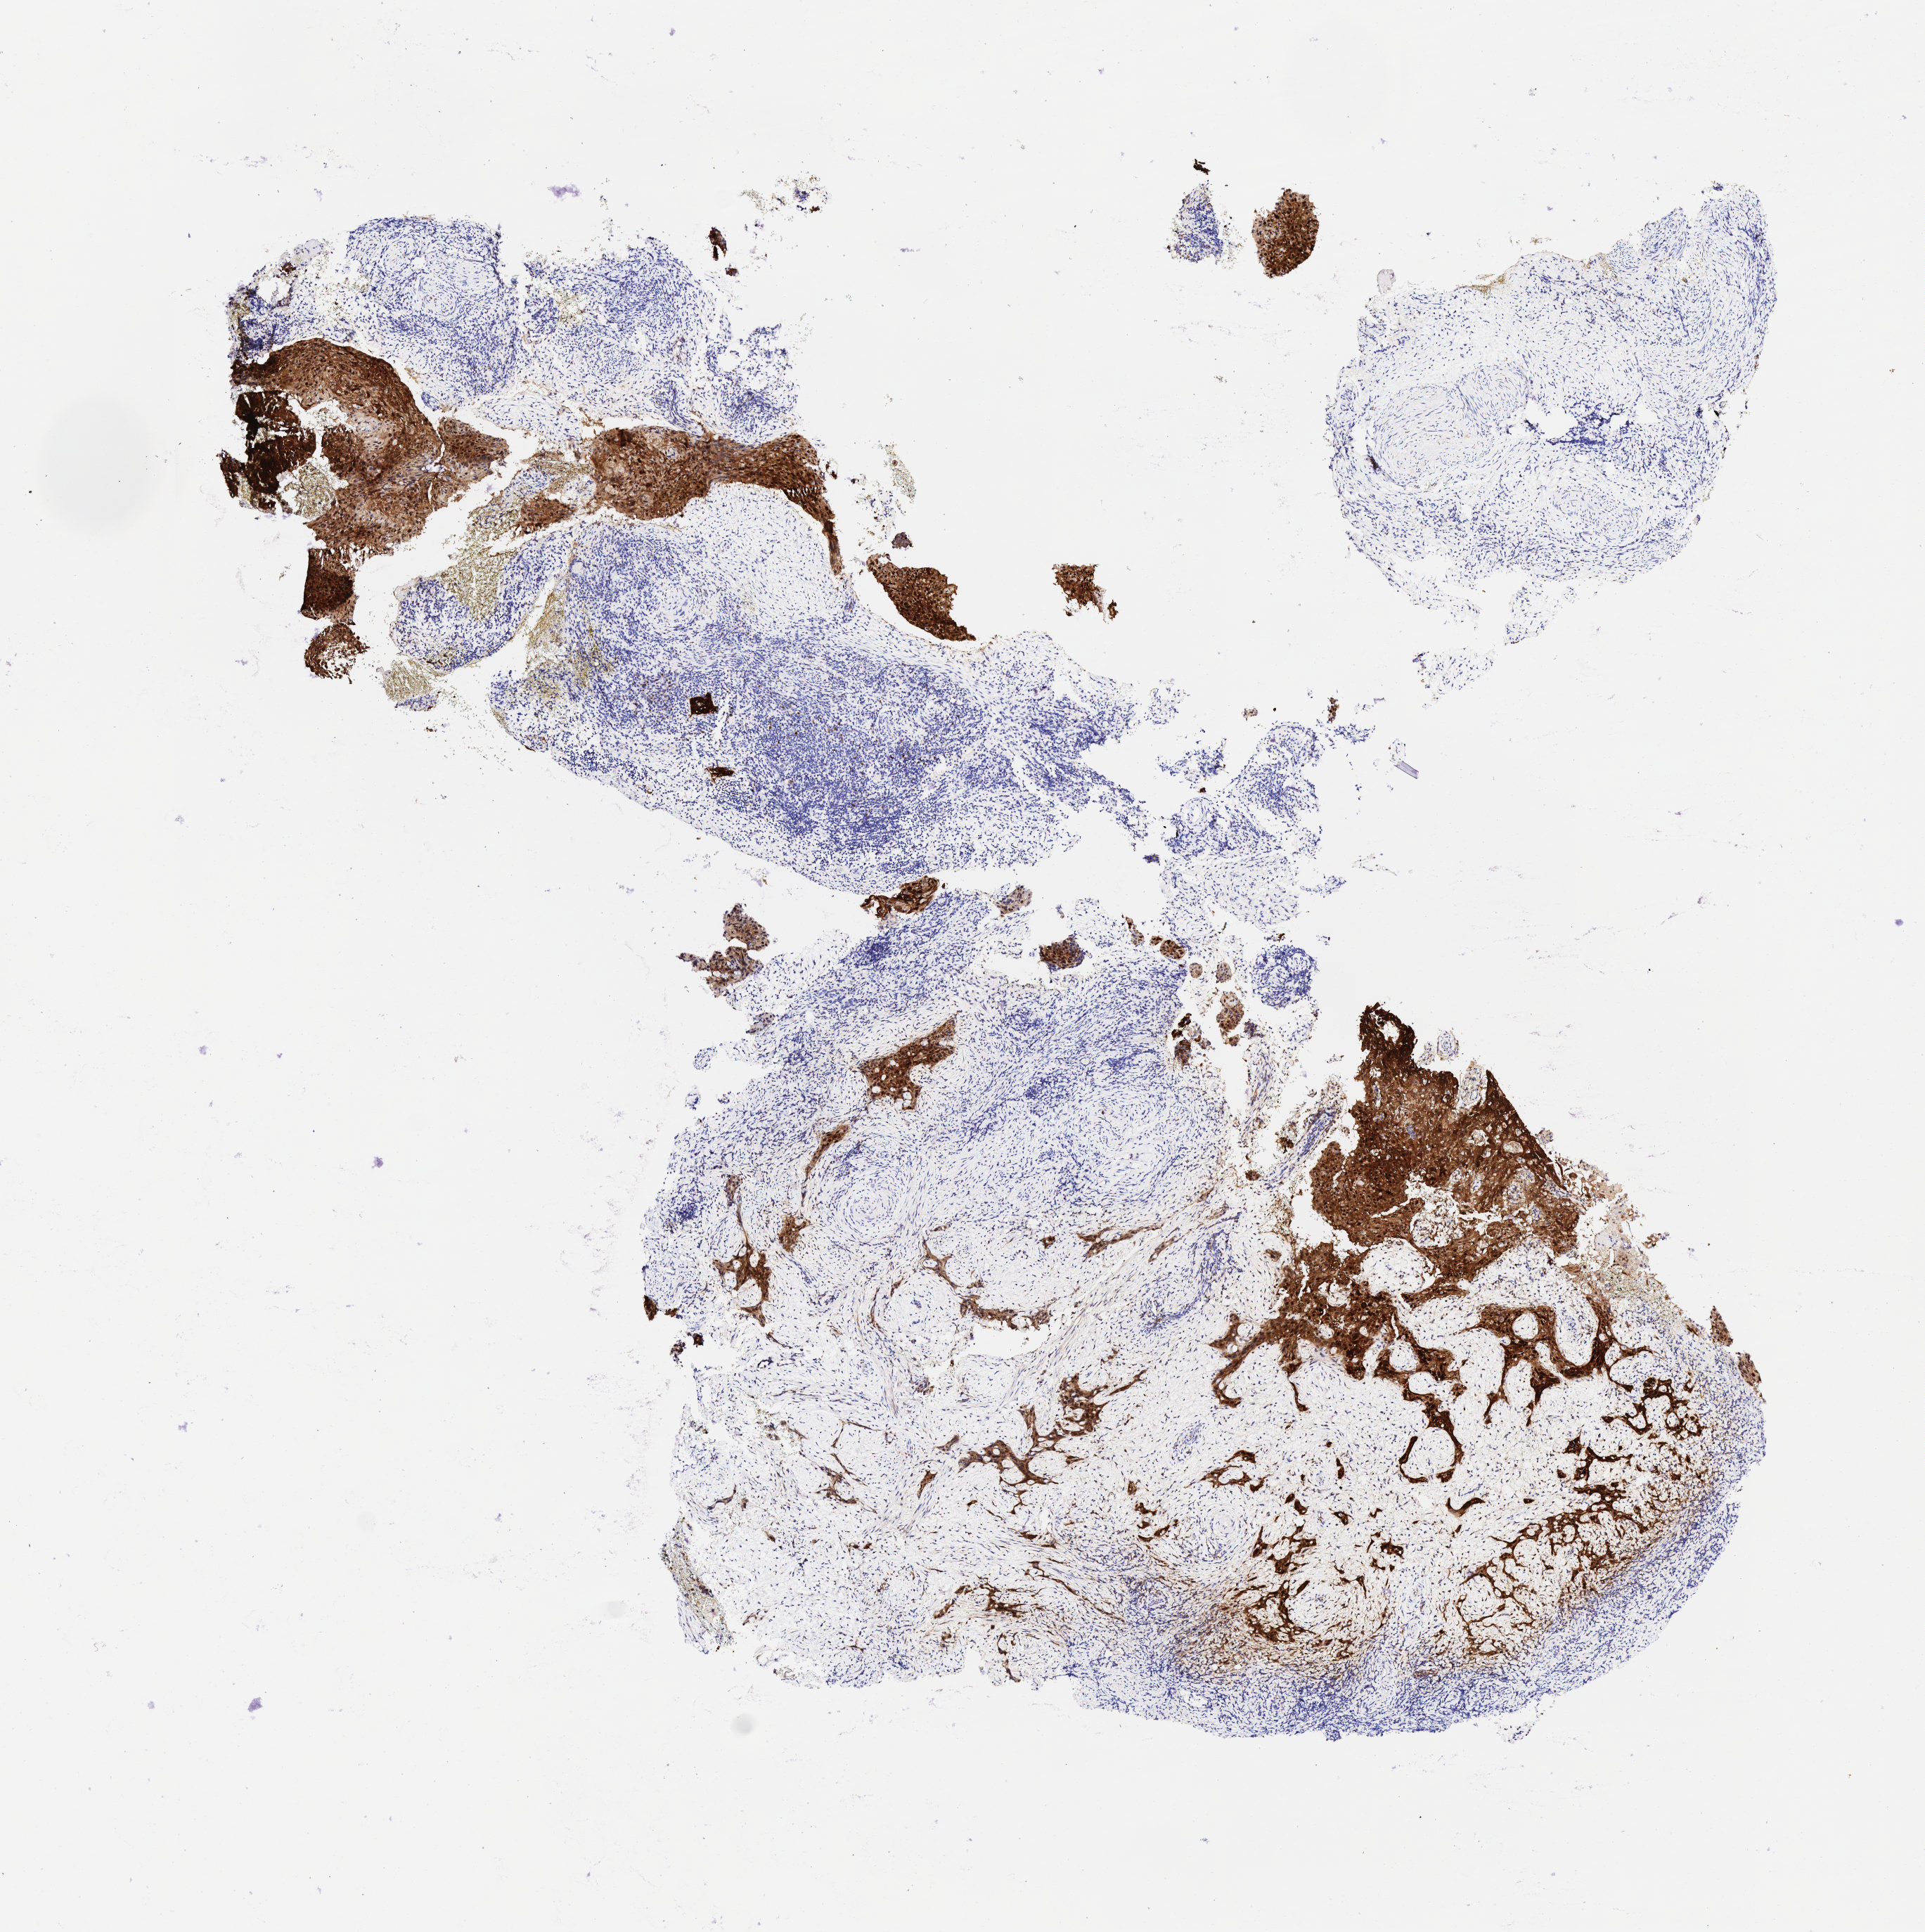
Immunohistochemistry (IHC) whole-slide image stained for p16 (p16INK4a) — shown as a low-resolution overview of the whole scanned area (about 5.5 x 5.6 mm). Tumor tissue. Anatomic site: cervix. Female patient, aged 57.
• histologic diagnosis: Squamous cell carcinoma, large cell, nonkeratinizing, NOS